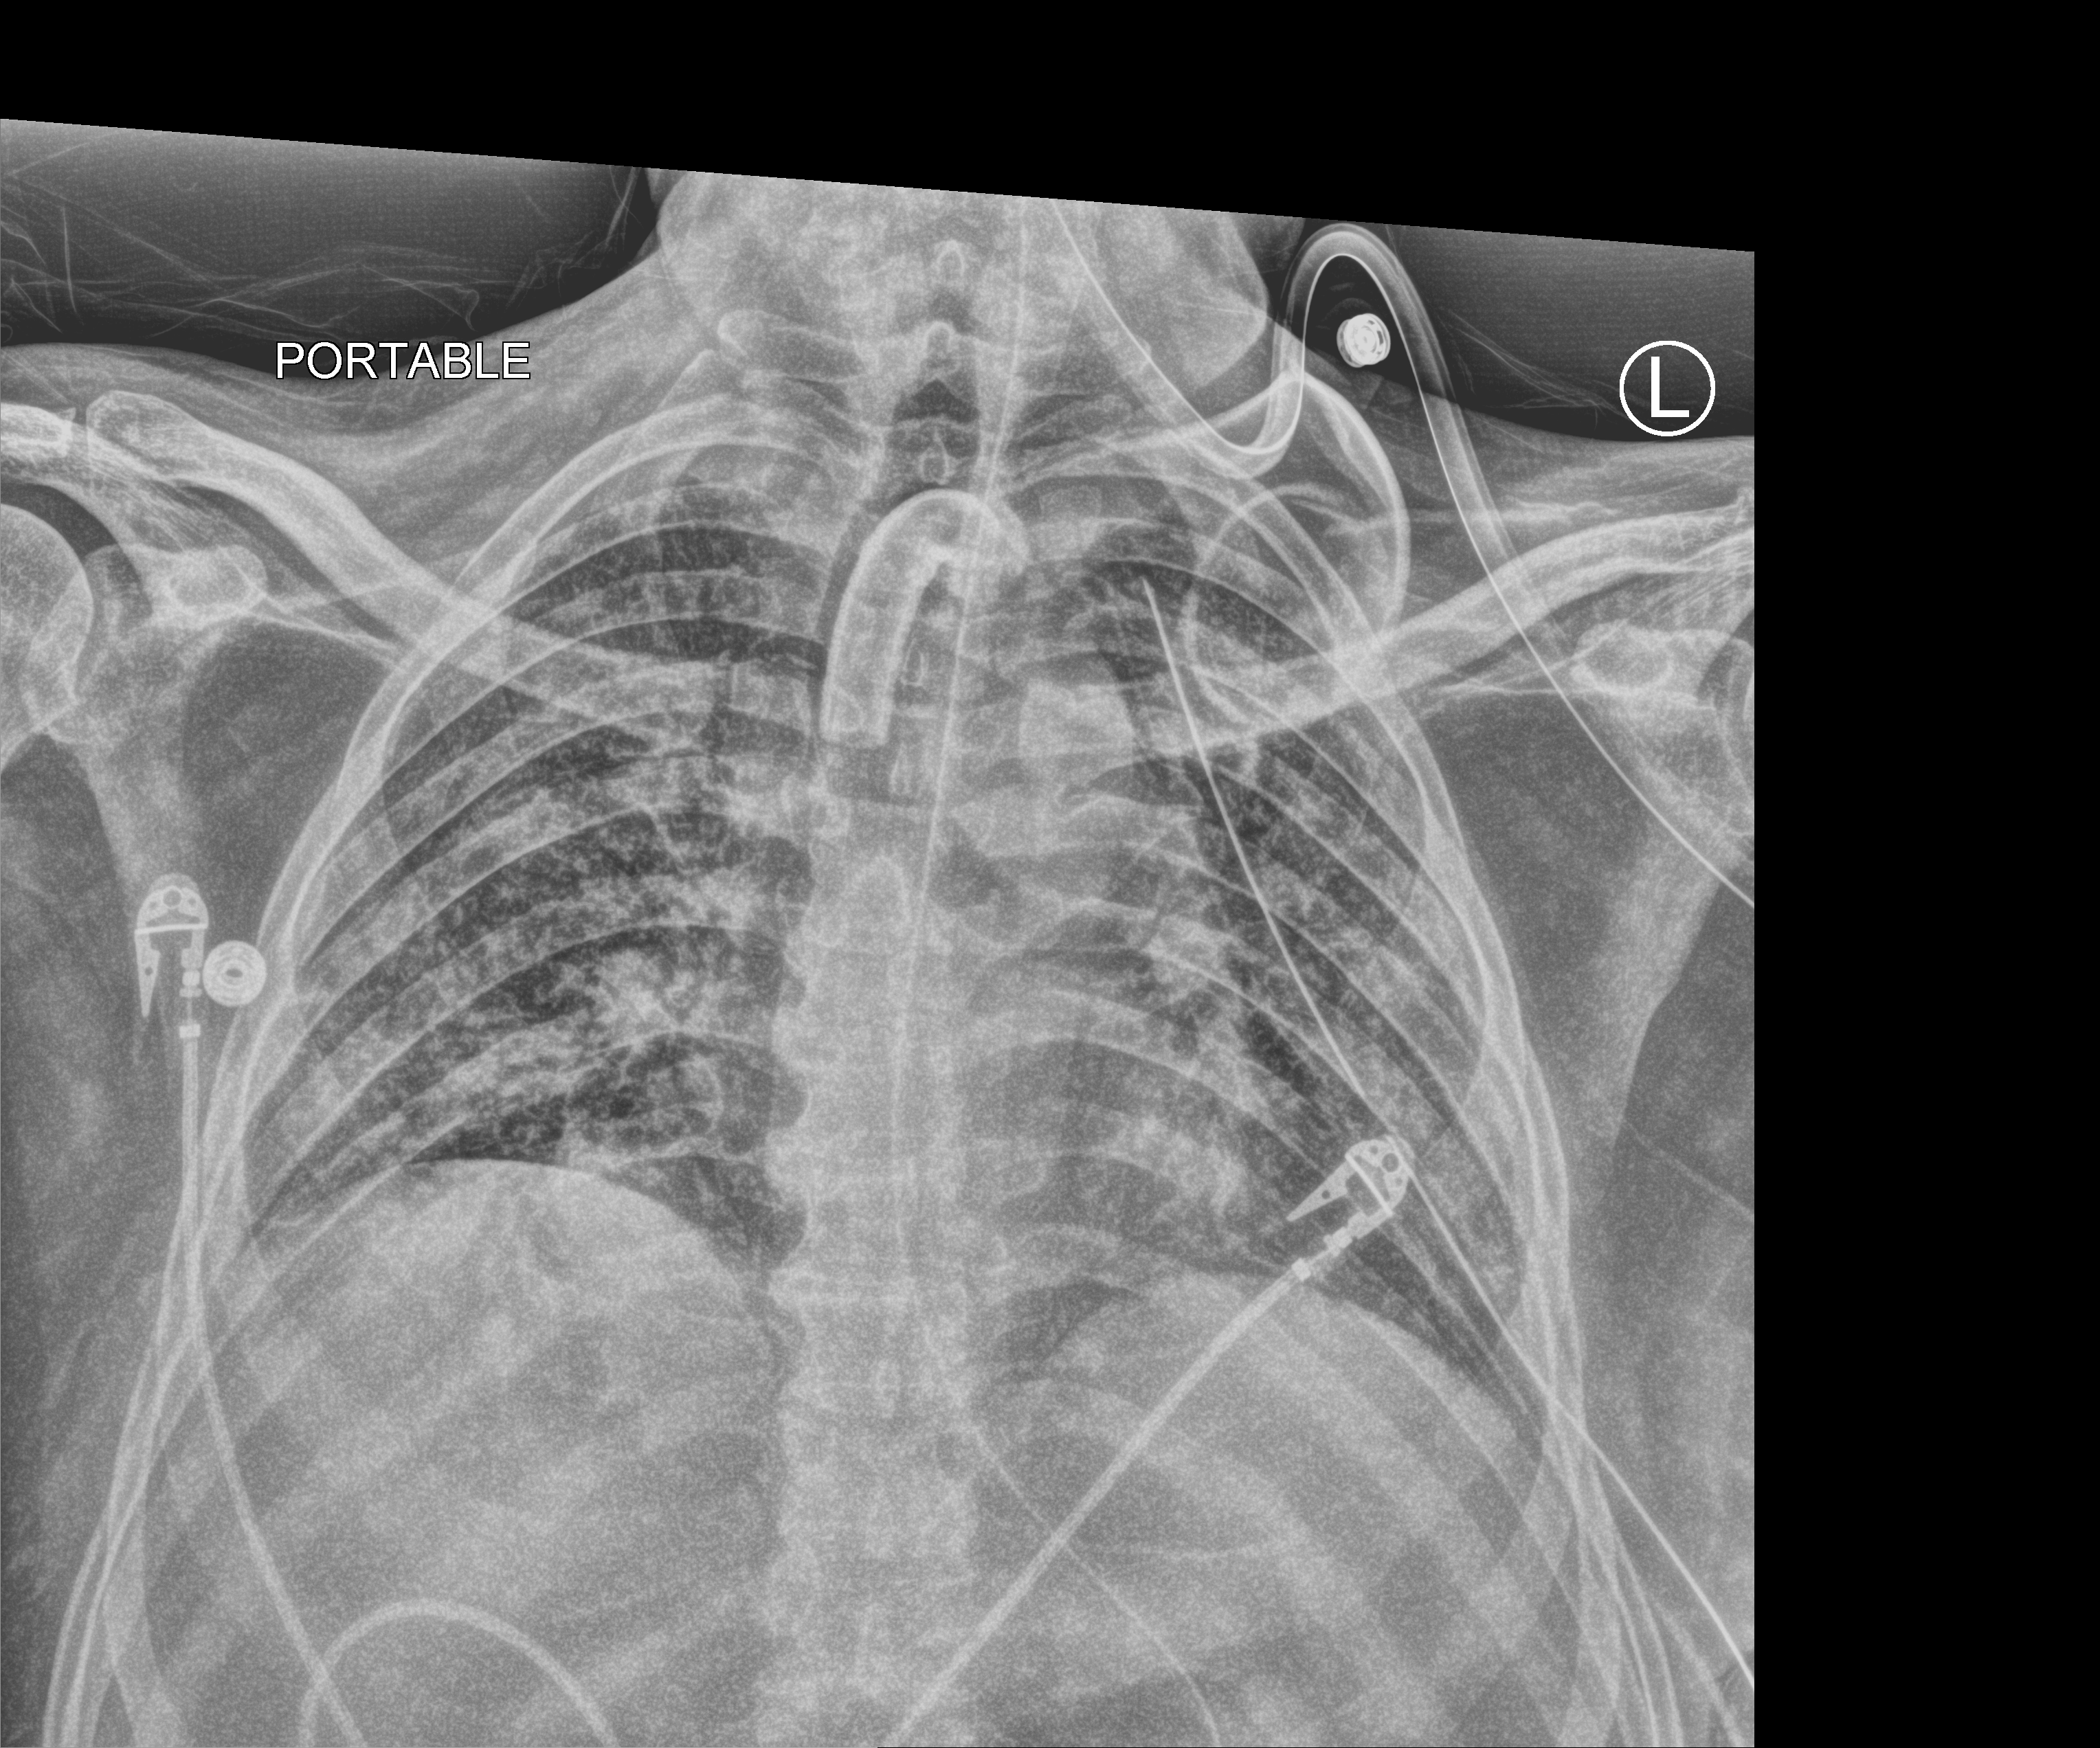
Chest X-ray (portable), anteroposterior (AP) projection. Patient hospitalised with COVID-19; male, aged 18–59 years.
Admission-level facts for this patient (not findings on this image; timing relative to this image not recorded):
- mechanically ventilated during this hospital stay: yes
- COPD (admission record): no
- length of hospital stay: 83 days